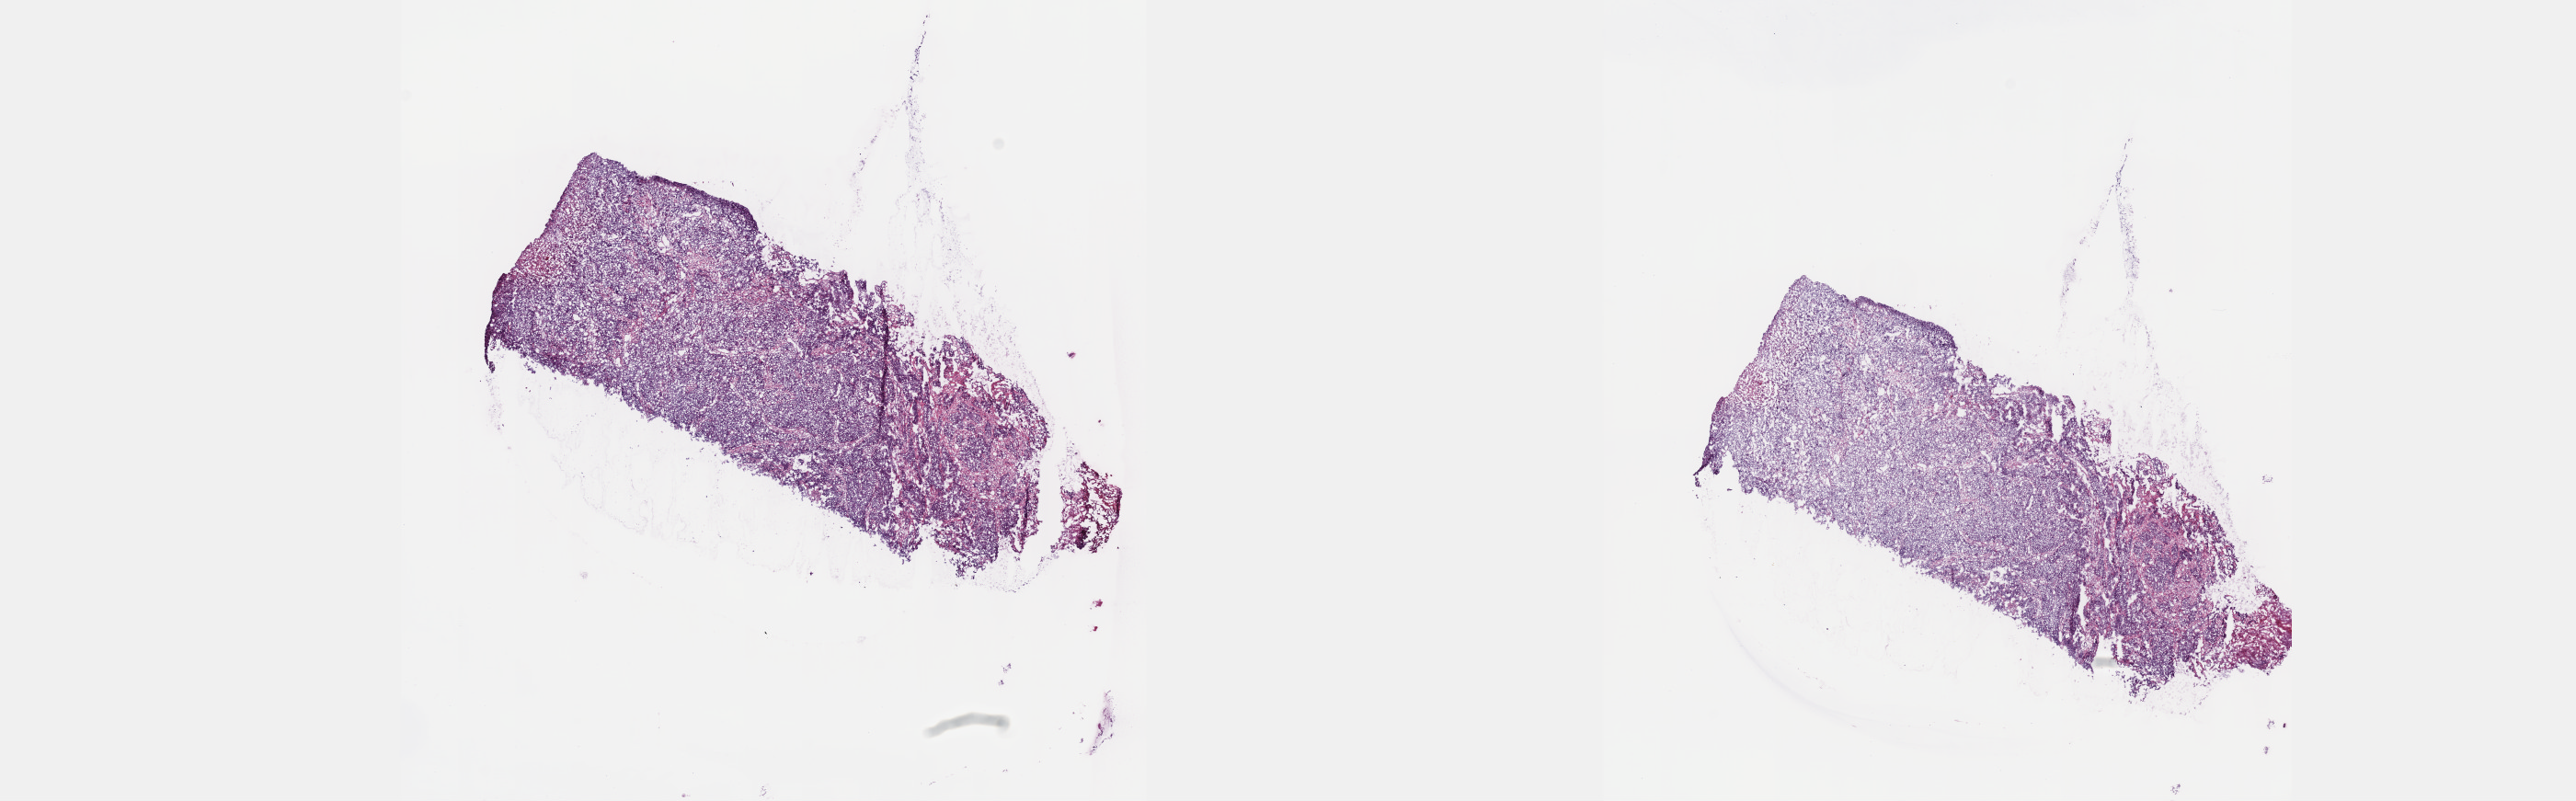
Digitized Hematoxylin and eosin (H&E) stained tissue section (whole slide), a low-resolution overview of the entire scanned area, about 22.6 x 7.0 mm; frozen section from the top of the tissue portion; sample: primary tumour, cervix. Female patient; age at initial diagnosis 47 years. Histologic grade: GX (grade cannot be assessed). Slide review estimates, as recorded: tumour cells 80%, tumour nuclei 80%, normal cells 0%, stromal cells 15%, necrosis 5%. Inflammatory infiltration, as recorded: lymphocyte infiltration 40%, monocyte infiltration 20%, neutrophil infiltration 20%.
* histologic diagnosis: Squamous cell carcinoma, NOS (cervix uteri)
* FIGO stage: IIB